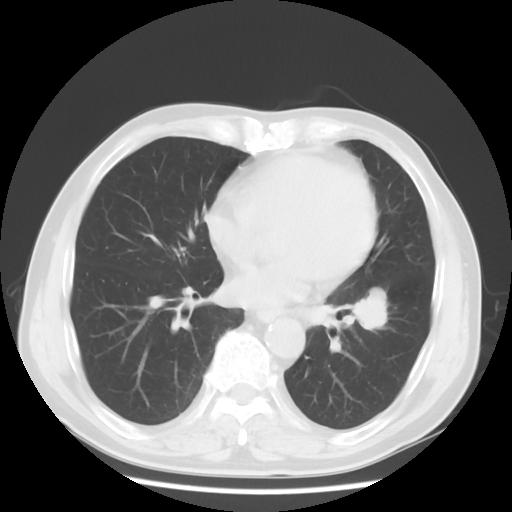
Chest CT, one axial slice; slice 28 of 68 in the series (ordered by position); reconstruction kernel STANDARD; lung window (W 1500 / L -600 HU); 5 mm slice thickness; 512 × 512 image matrix, field of view 360 × 360 mm. Patient: male, 71 years. From the clinical record (not read from this slice): clinical TNM (as recorded): T1c N1 M0; histopathological grade: G2-3.
Structures marked on this image (rectangle marked by the reading radiologist):
- lung tumour (recorded histology: adenocarcinoma): box from (x=354, y=280) to (x=401, y=338) px